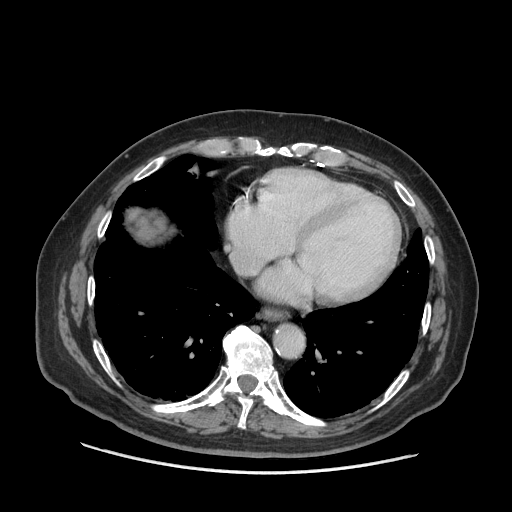
Contrast-enhanced abdominal CT (liver protocol), one axial slice; slice 68 of 77 in the series (ordered by position); soft-tissue window (W 400 / L 40 HU); 2.5 mm slice thickness; 512 × 512 image matrix, field of view 420 × 420 mm. Case-level facts recorded for this patient, not image findings: diagnosis: hepatocellular carcinoma (patient treated with transarterial chemoembolisation; whether this scan precedes or follows treatment is not stated here); TNM stage (as recorded): Stage-I; Child-Pugh class: A; tumour differentiation: well differentiated; tumour size: 3.8 cm.
Annotated regions visible in this slice (semi-automatic segmentation, software-assisted and operator-edited):
- liver parenchyma outside the tumour (the mass and vessels are separate outlines, so this box may not span the whole liver): bounding box [x1, y1, x2, y2] px = [136, 212, 171, 240]